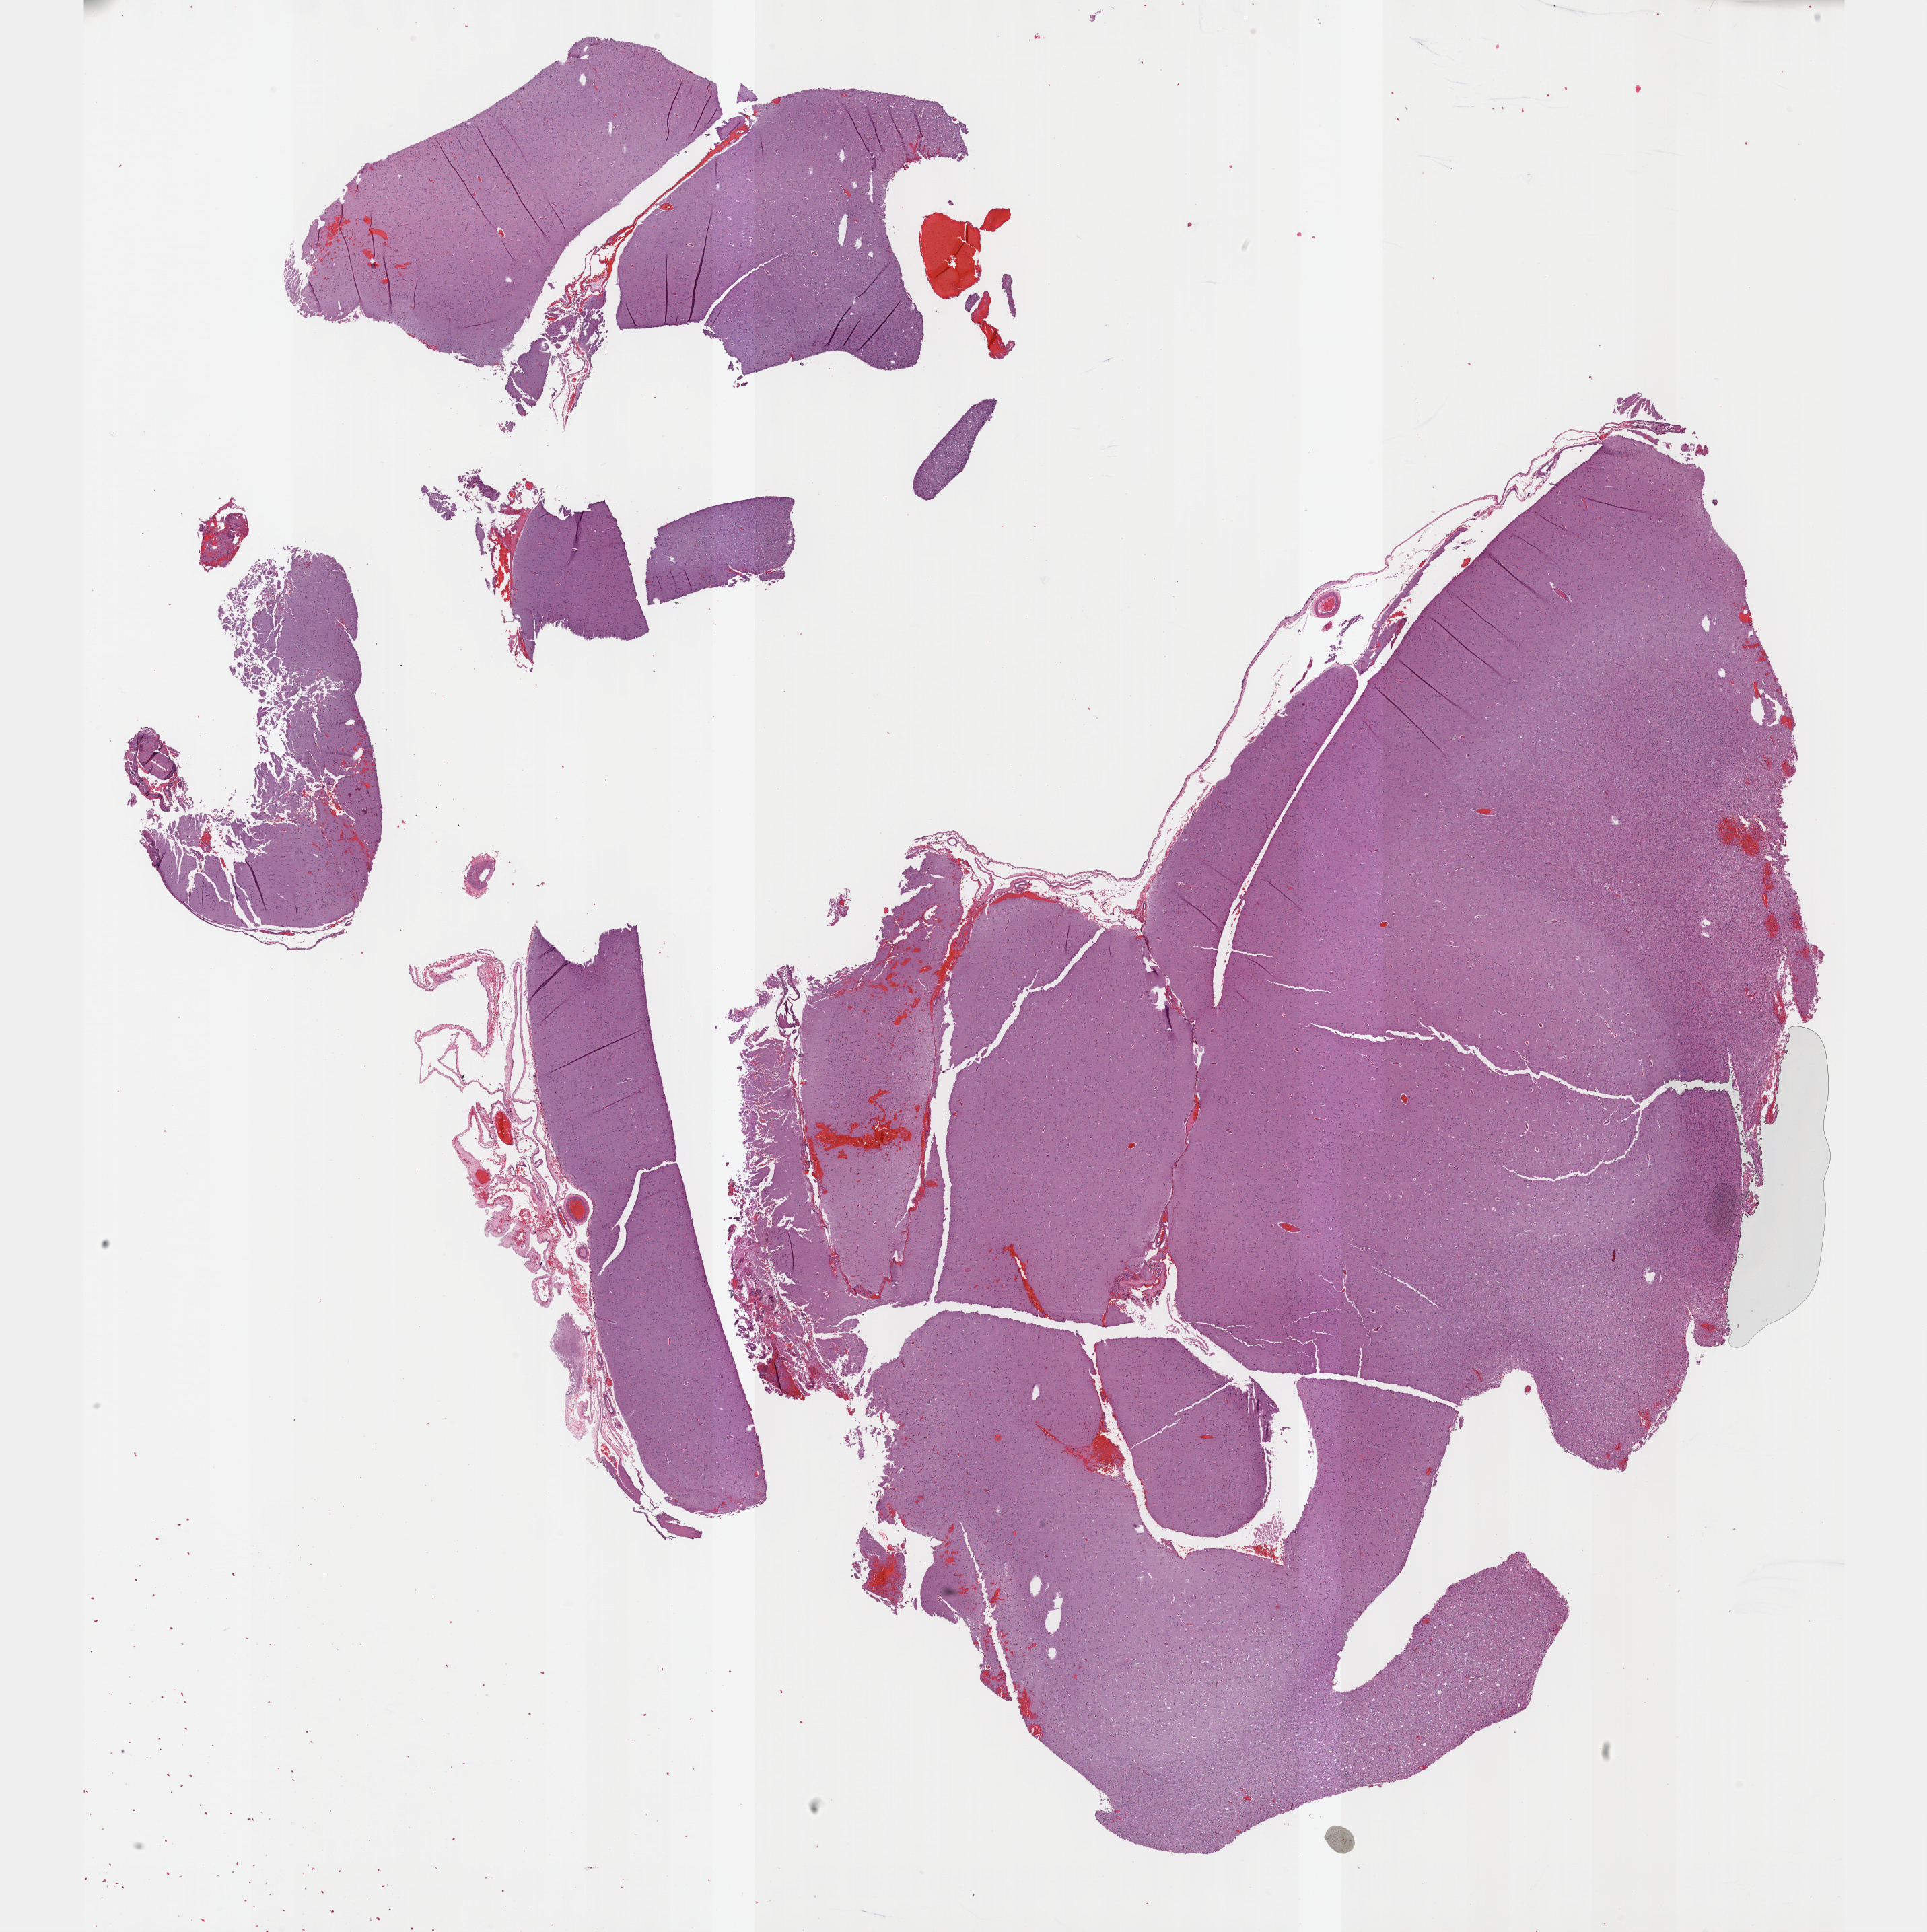
H&E-stained whole-slide image, low-resolution overview of the scanned area, about 23.1 x 23.2 mm; formalin-fixed paraffin-embedded (FFPE) diagnostic section; brain, primary tumour sample. Male patient; age at initial diagnosis 35 years. Histologic grade: G3 (poorly differentiated).
Histologic diagnosis: Oligodendroglioma, anaplastic (cerebrum).